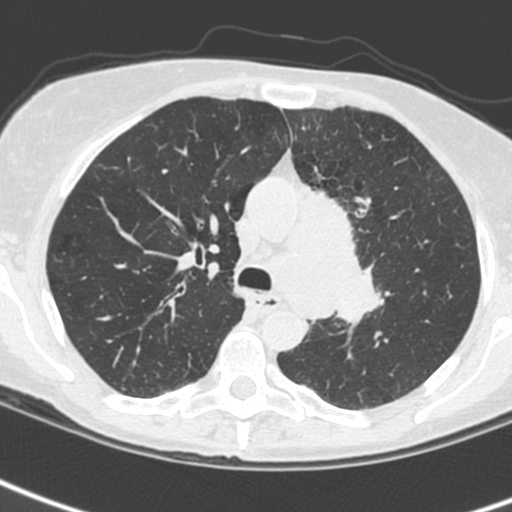
Low-dose screening chest CT, one axial slice. Slice 167 of 242 in the series (ordered by position). 120 kVp. Lung window (W 1500 / L -600 HU). 1.3 mm slice thickness. 512 × 512 image matrix, field of view 284 × 284 mm.
Structures marked on this image (expert manual segmentation):
- lesion 3 (tumor, upper lobe of left lung): bounding box (x1, y1, x2, y2) in pixels: (306, 189, 382, 326)